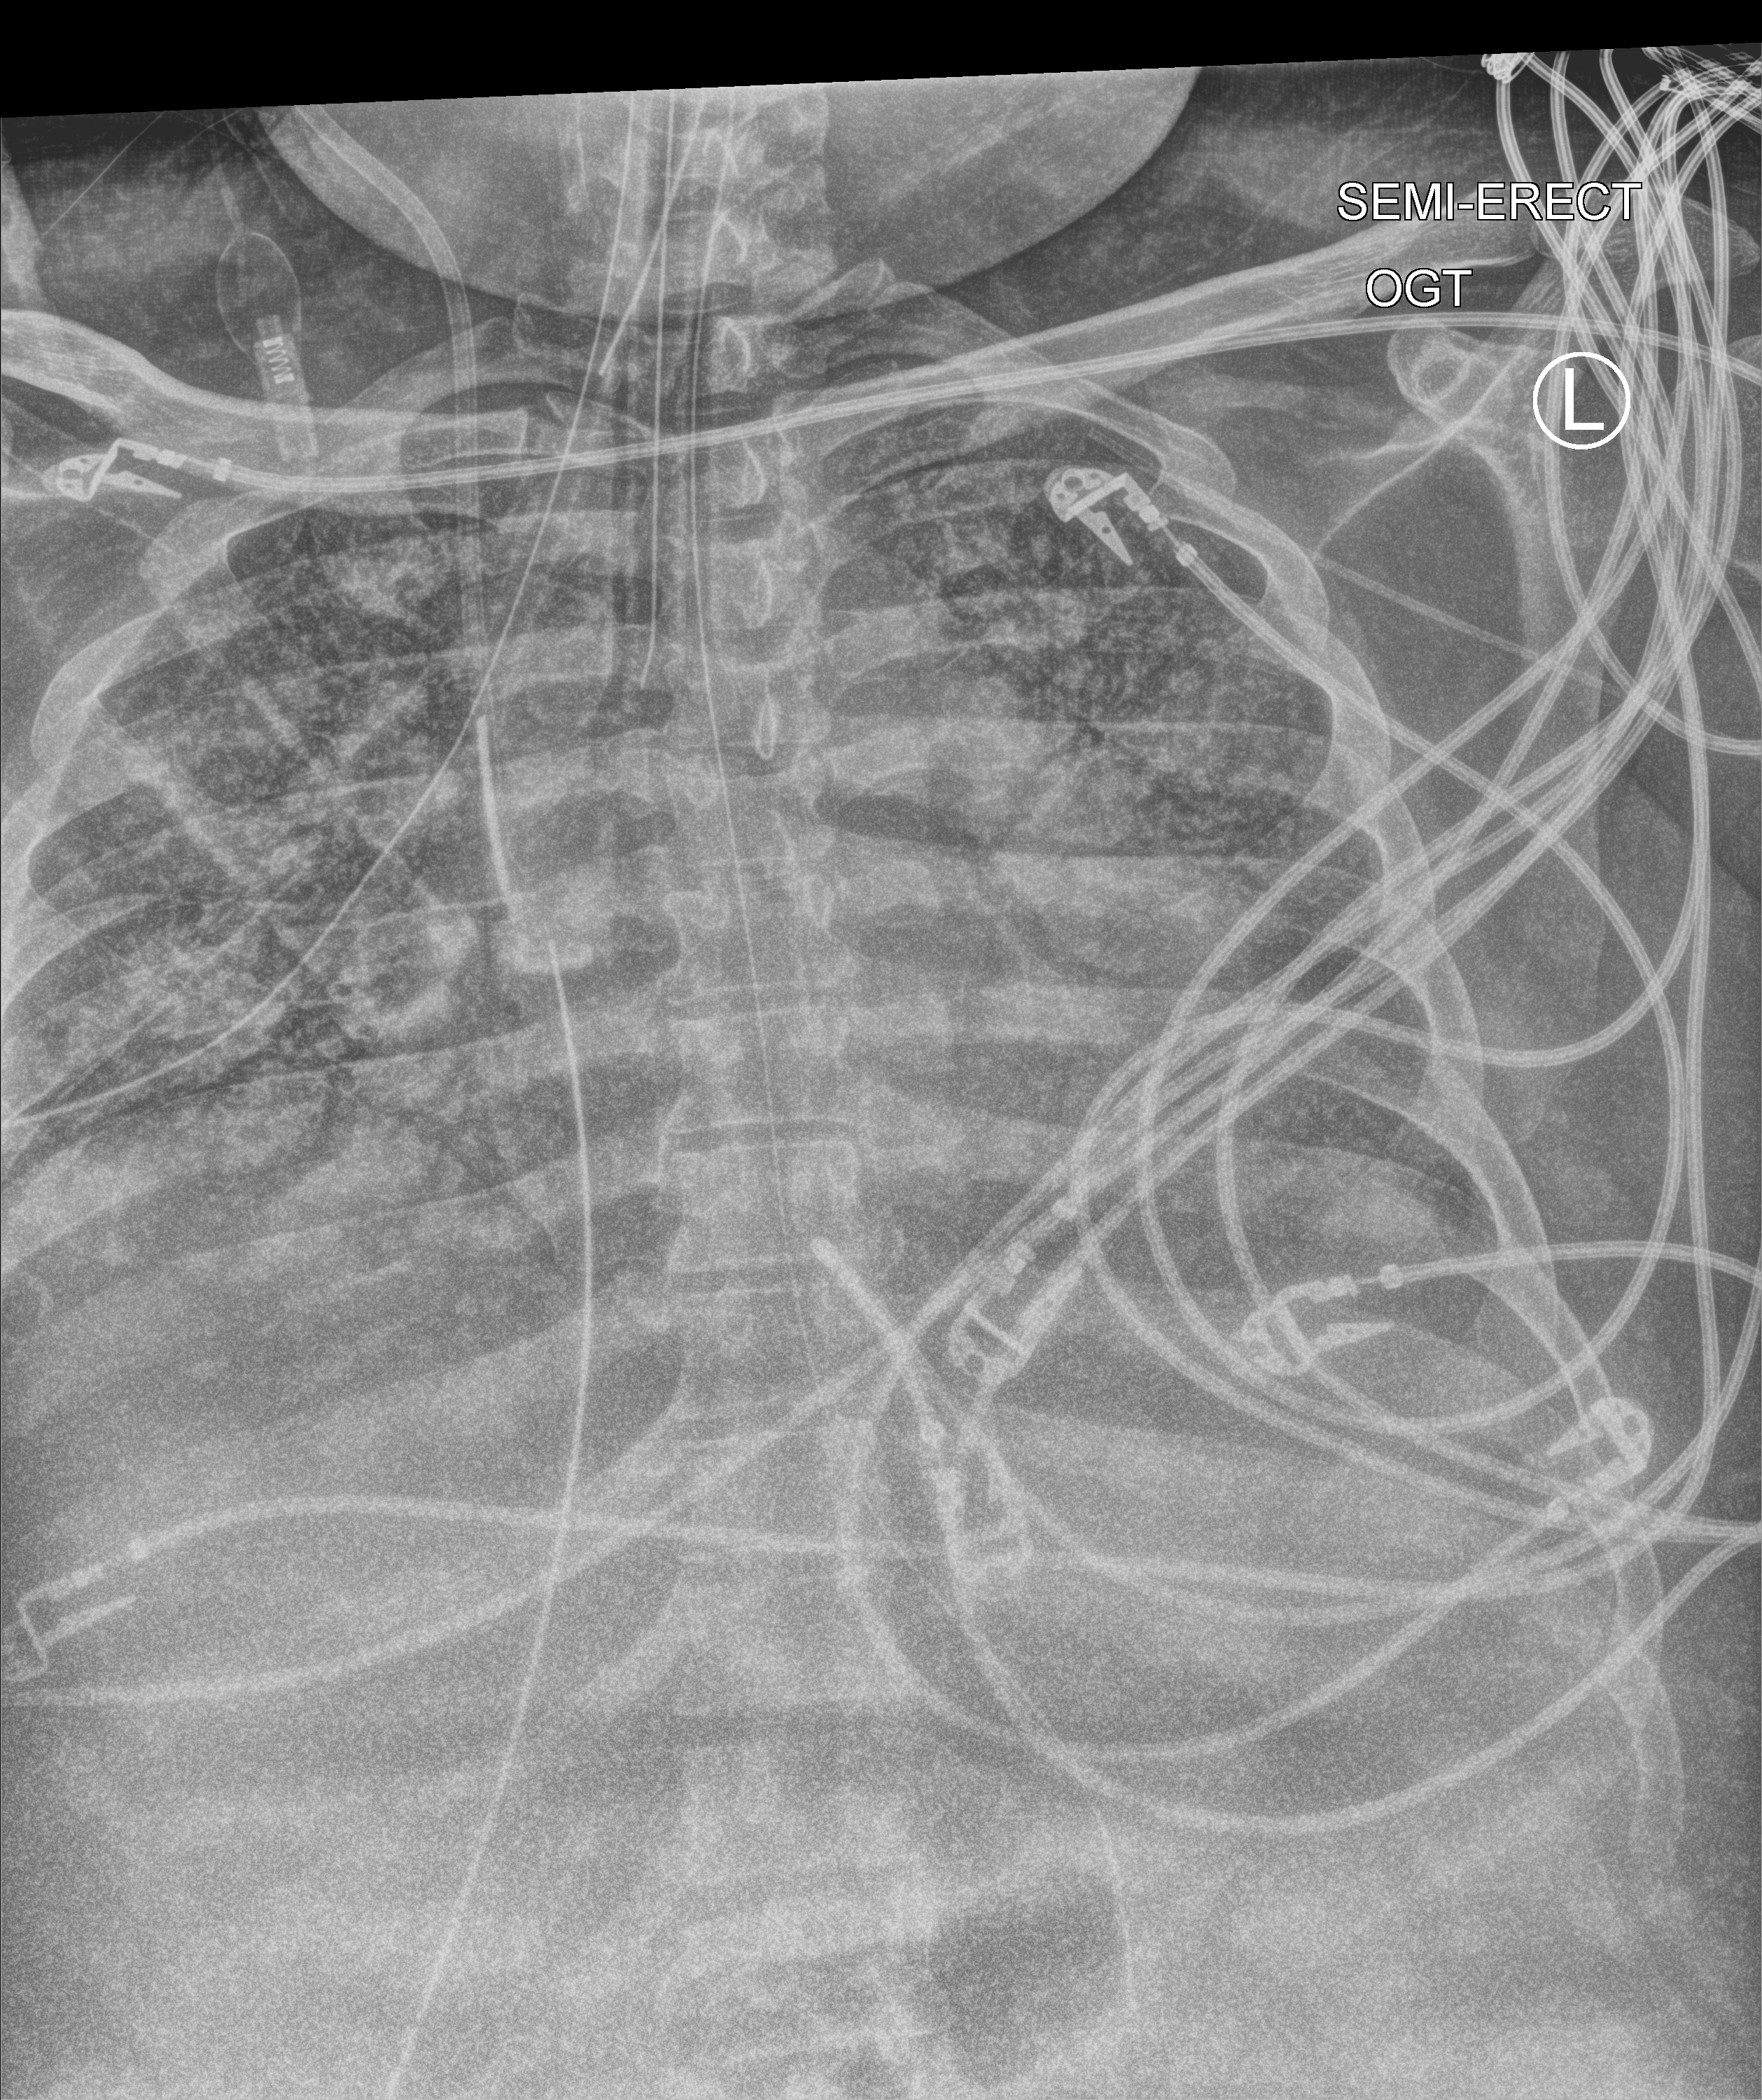
Chest X-ray (portable); anteroposterior (AP) projection. Patient hospitalised with COVID-19, aged 18–59 years.
From the hospital-stay record, not from the radiograph (when in the stay this image was taken is not recorded): length of hospital stay: 22 days; mechanically ventilated during this hospital stay: yes.